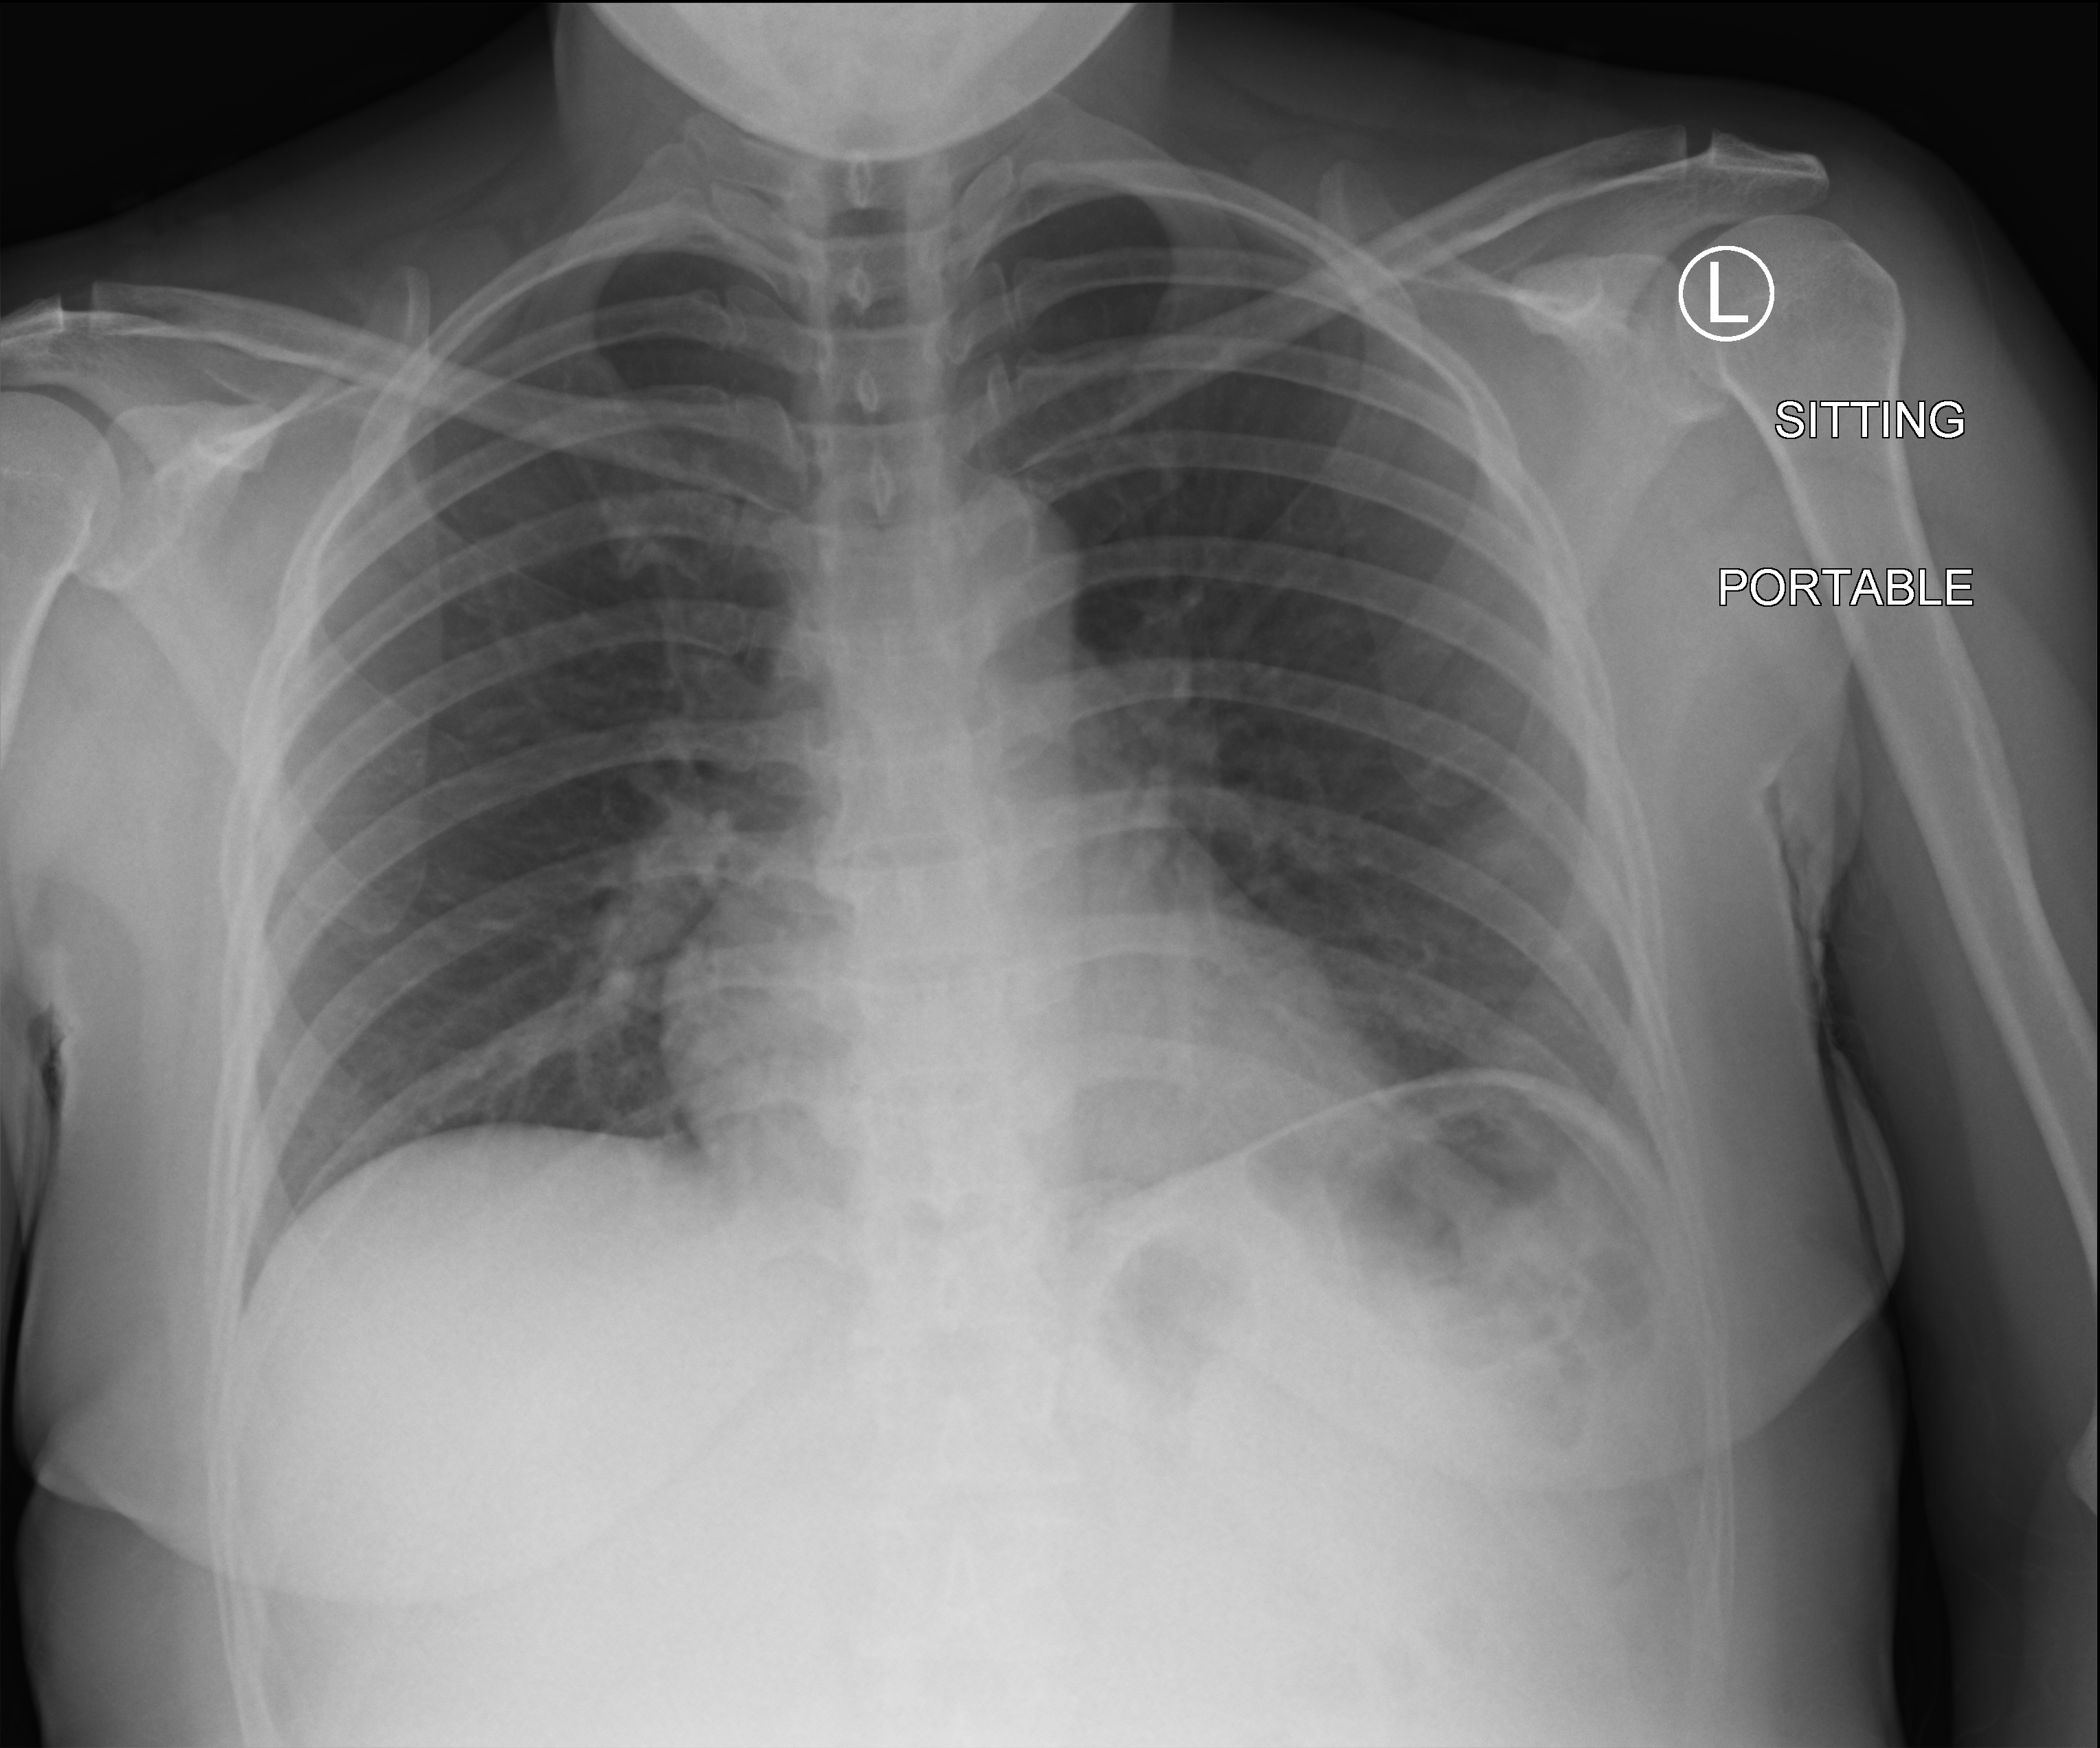
Chest X-ray (portable), anteroposterior (AP) projection. Female patient hospitalised with COVID-19, age 18–59 years.
Admission-level facts for this patient (not findings on this image; timing relative to this image not recorded): admitted to intensive care during this hospital stay: no.